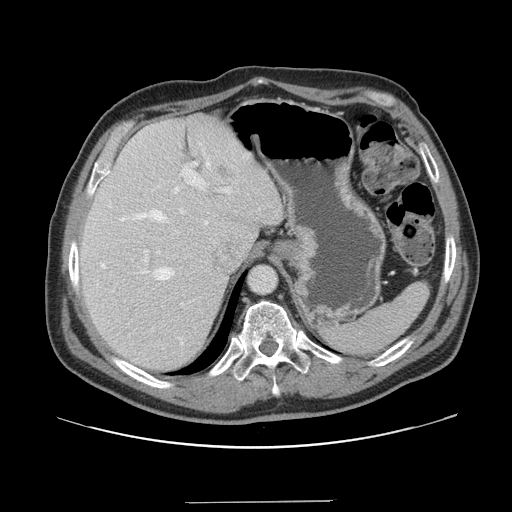
Contrast-enhanced abdominal CT, one axial slice. 120 kVp. Intravenous contrast given. Soft-tissue window (W 400 / L 40 HU). 2.5 mm slice thickness. 512 × 512 image matrix, field of view 399 × 399 mm. Male patient, age 63 years. From the clinical record (not read from this slice): diagnosis: colorectal cancer liver metastases, imaged before liver resection; multiple liver metastases: no; largest metastasis: 2.1 cm; disease in both lobes: no.
Outlined on this slice (outlined manually by an expert reader):
- hepatic veins: bounding box (x1, y1, x2, y2) in pixels: (101, 161, 210, 280)
- liver: (78, 114, 282, 372)
- planned liver remnant (the part of the liver to remain after resection): (79, 118, 264, 372)
- portal vein (with intrahepatic branches): (143, 162, 231, 305)
- liver metastasis: (217, 166, 229, 180)